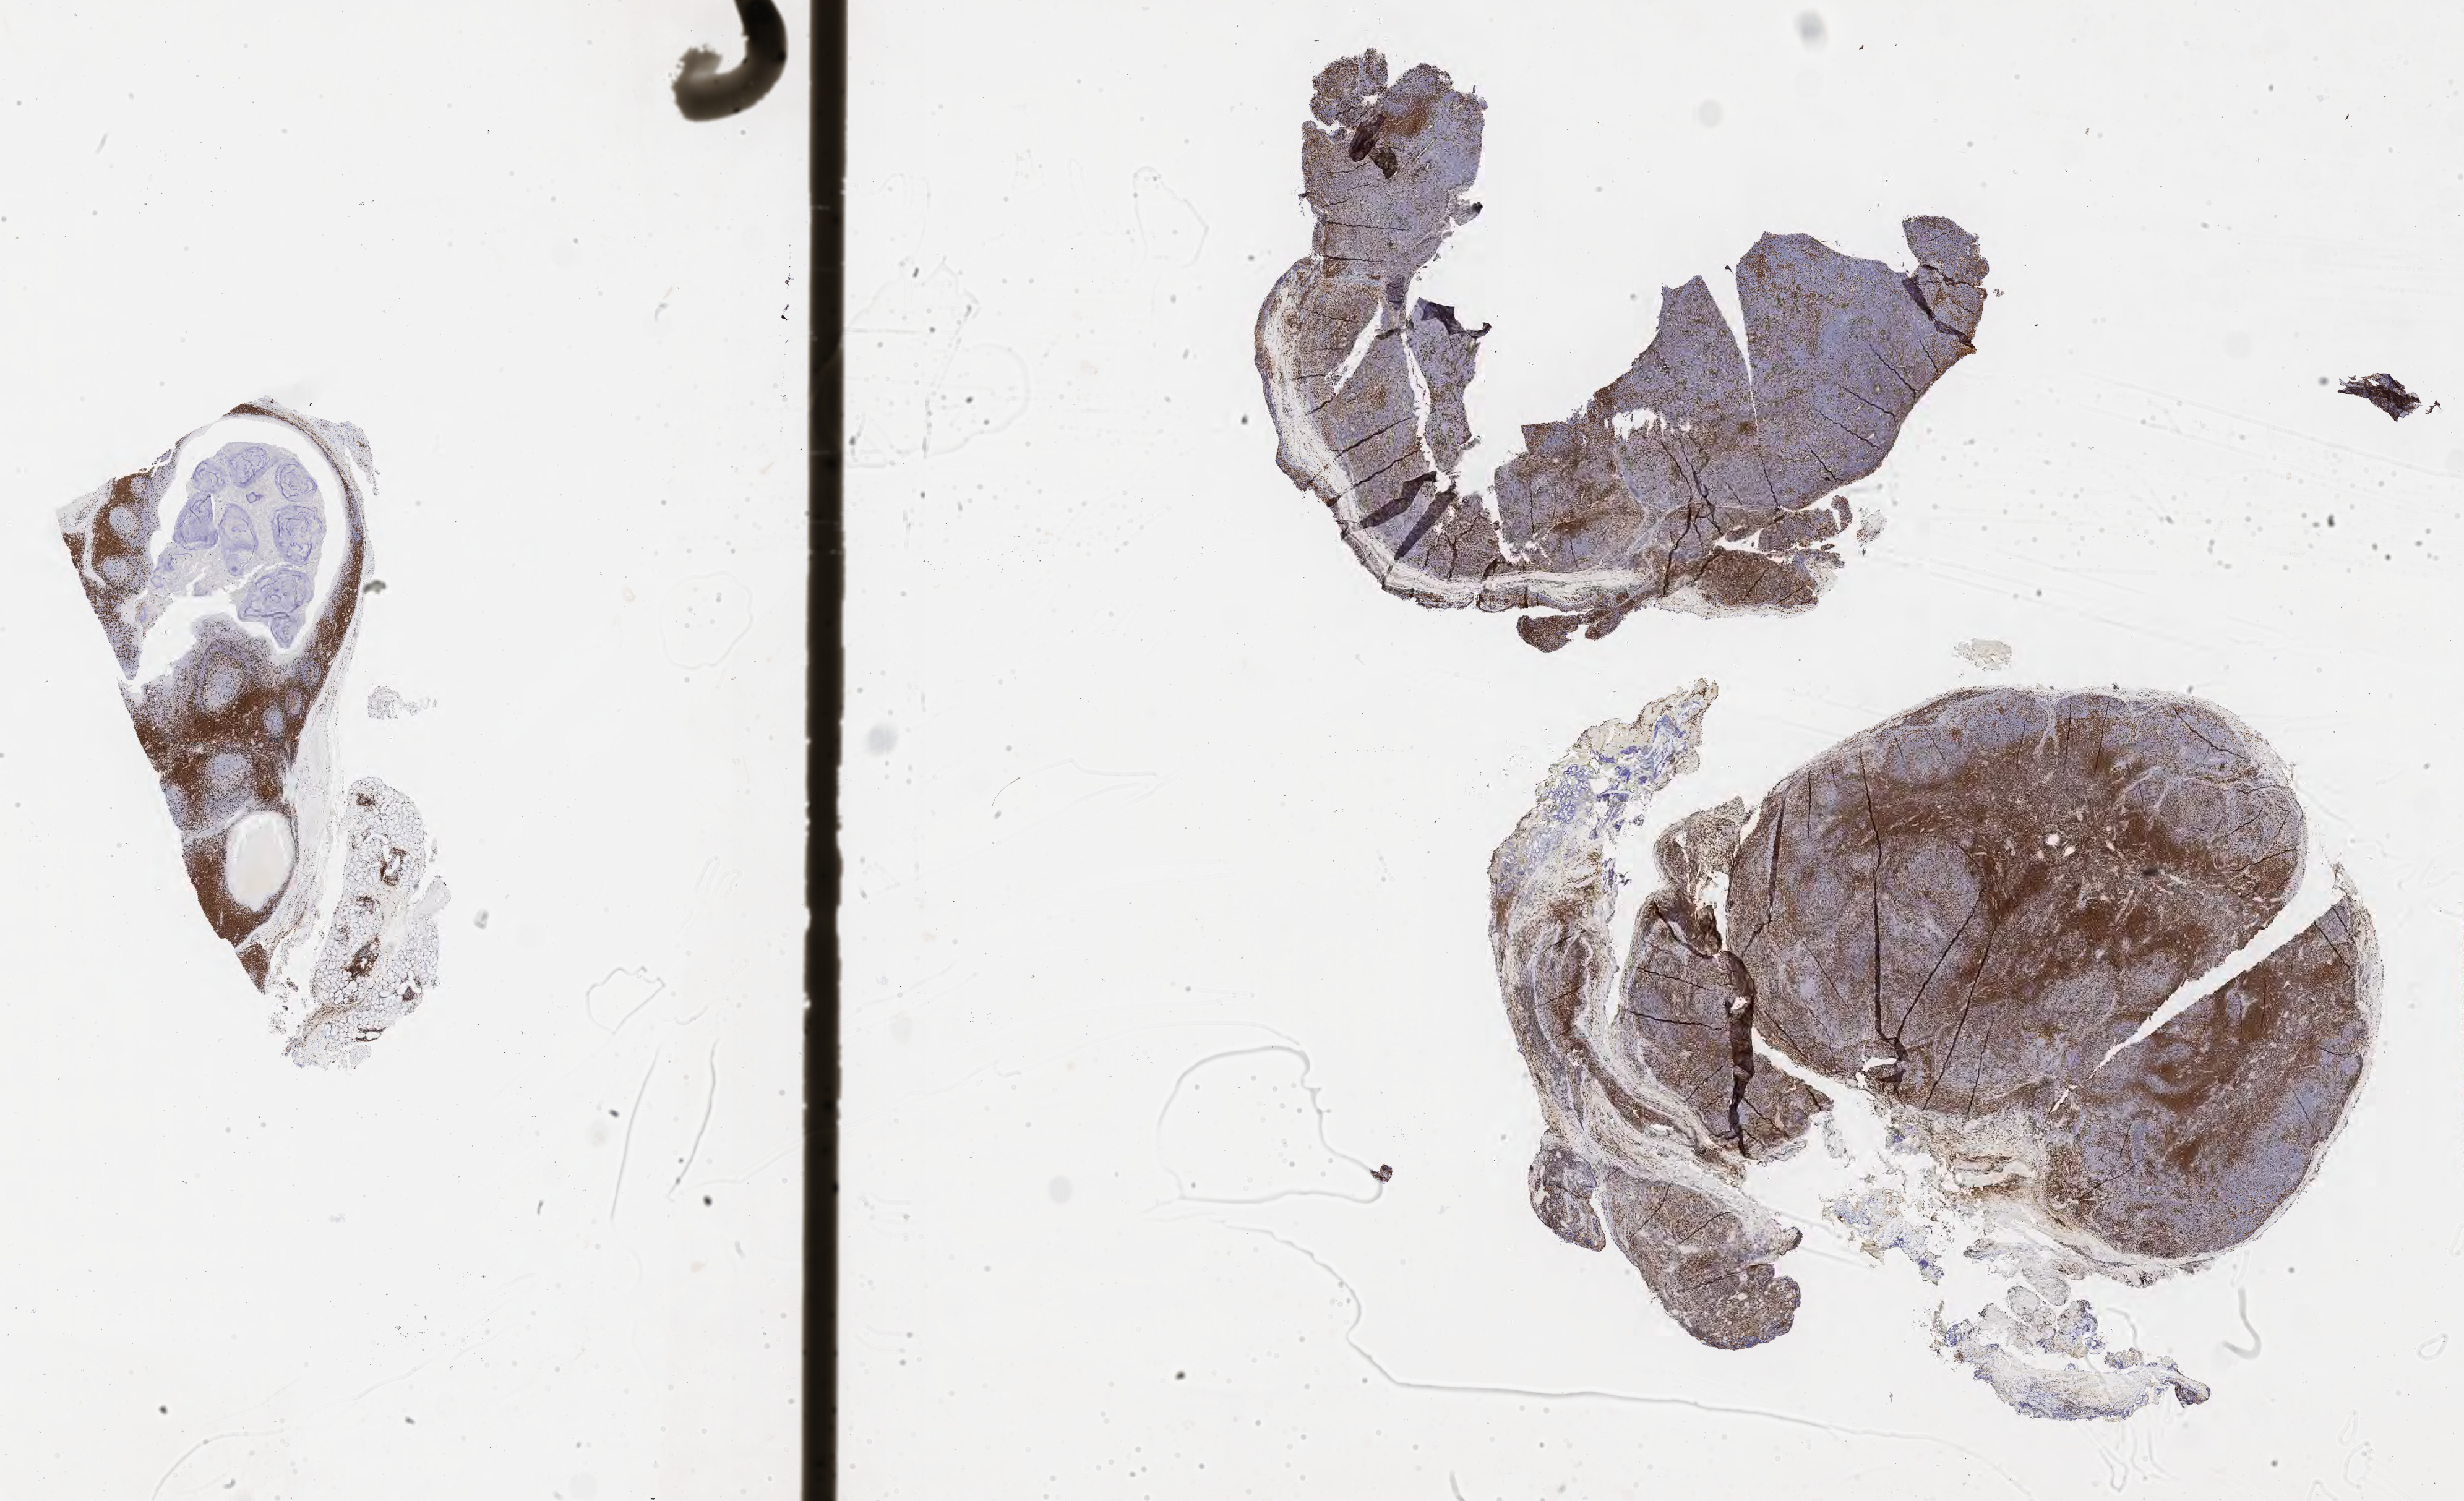
Whole-slide image, immunohistochemical stain for CD3, whole scanned area (about 32.2 x 19.6 mm) shown as a low-resolution overview, specimen: tumor tissue. Patient male; age 25 years.
Diagnosis: Burkitt lymphoma, NOS.